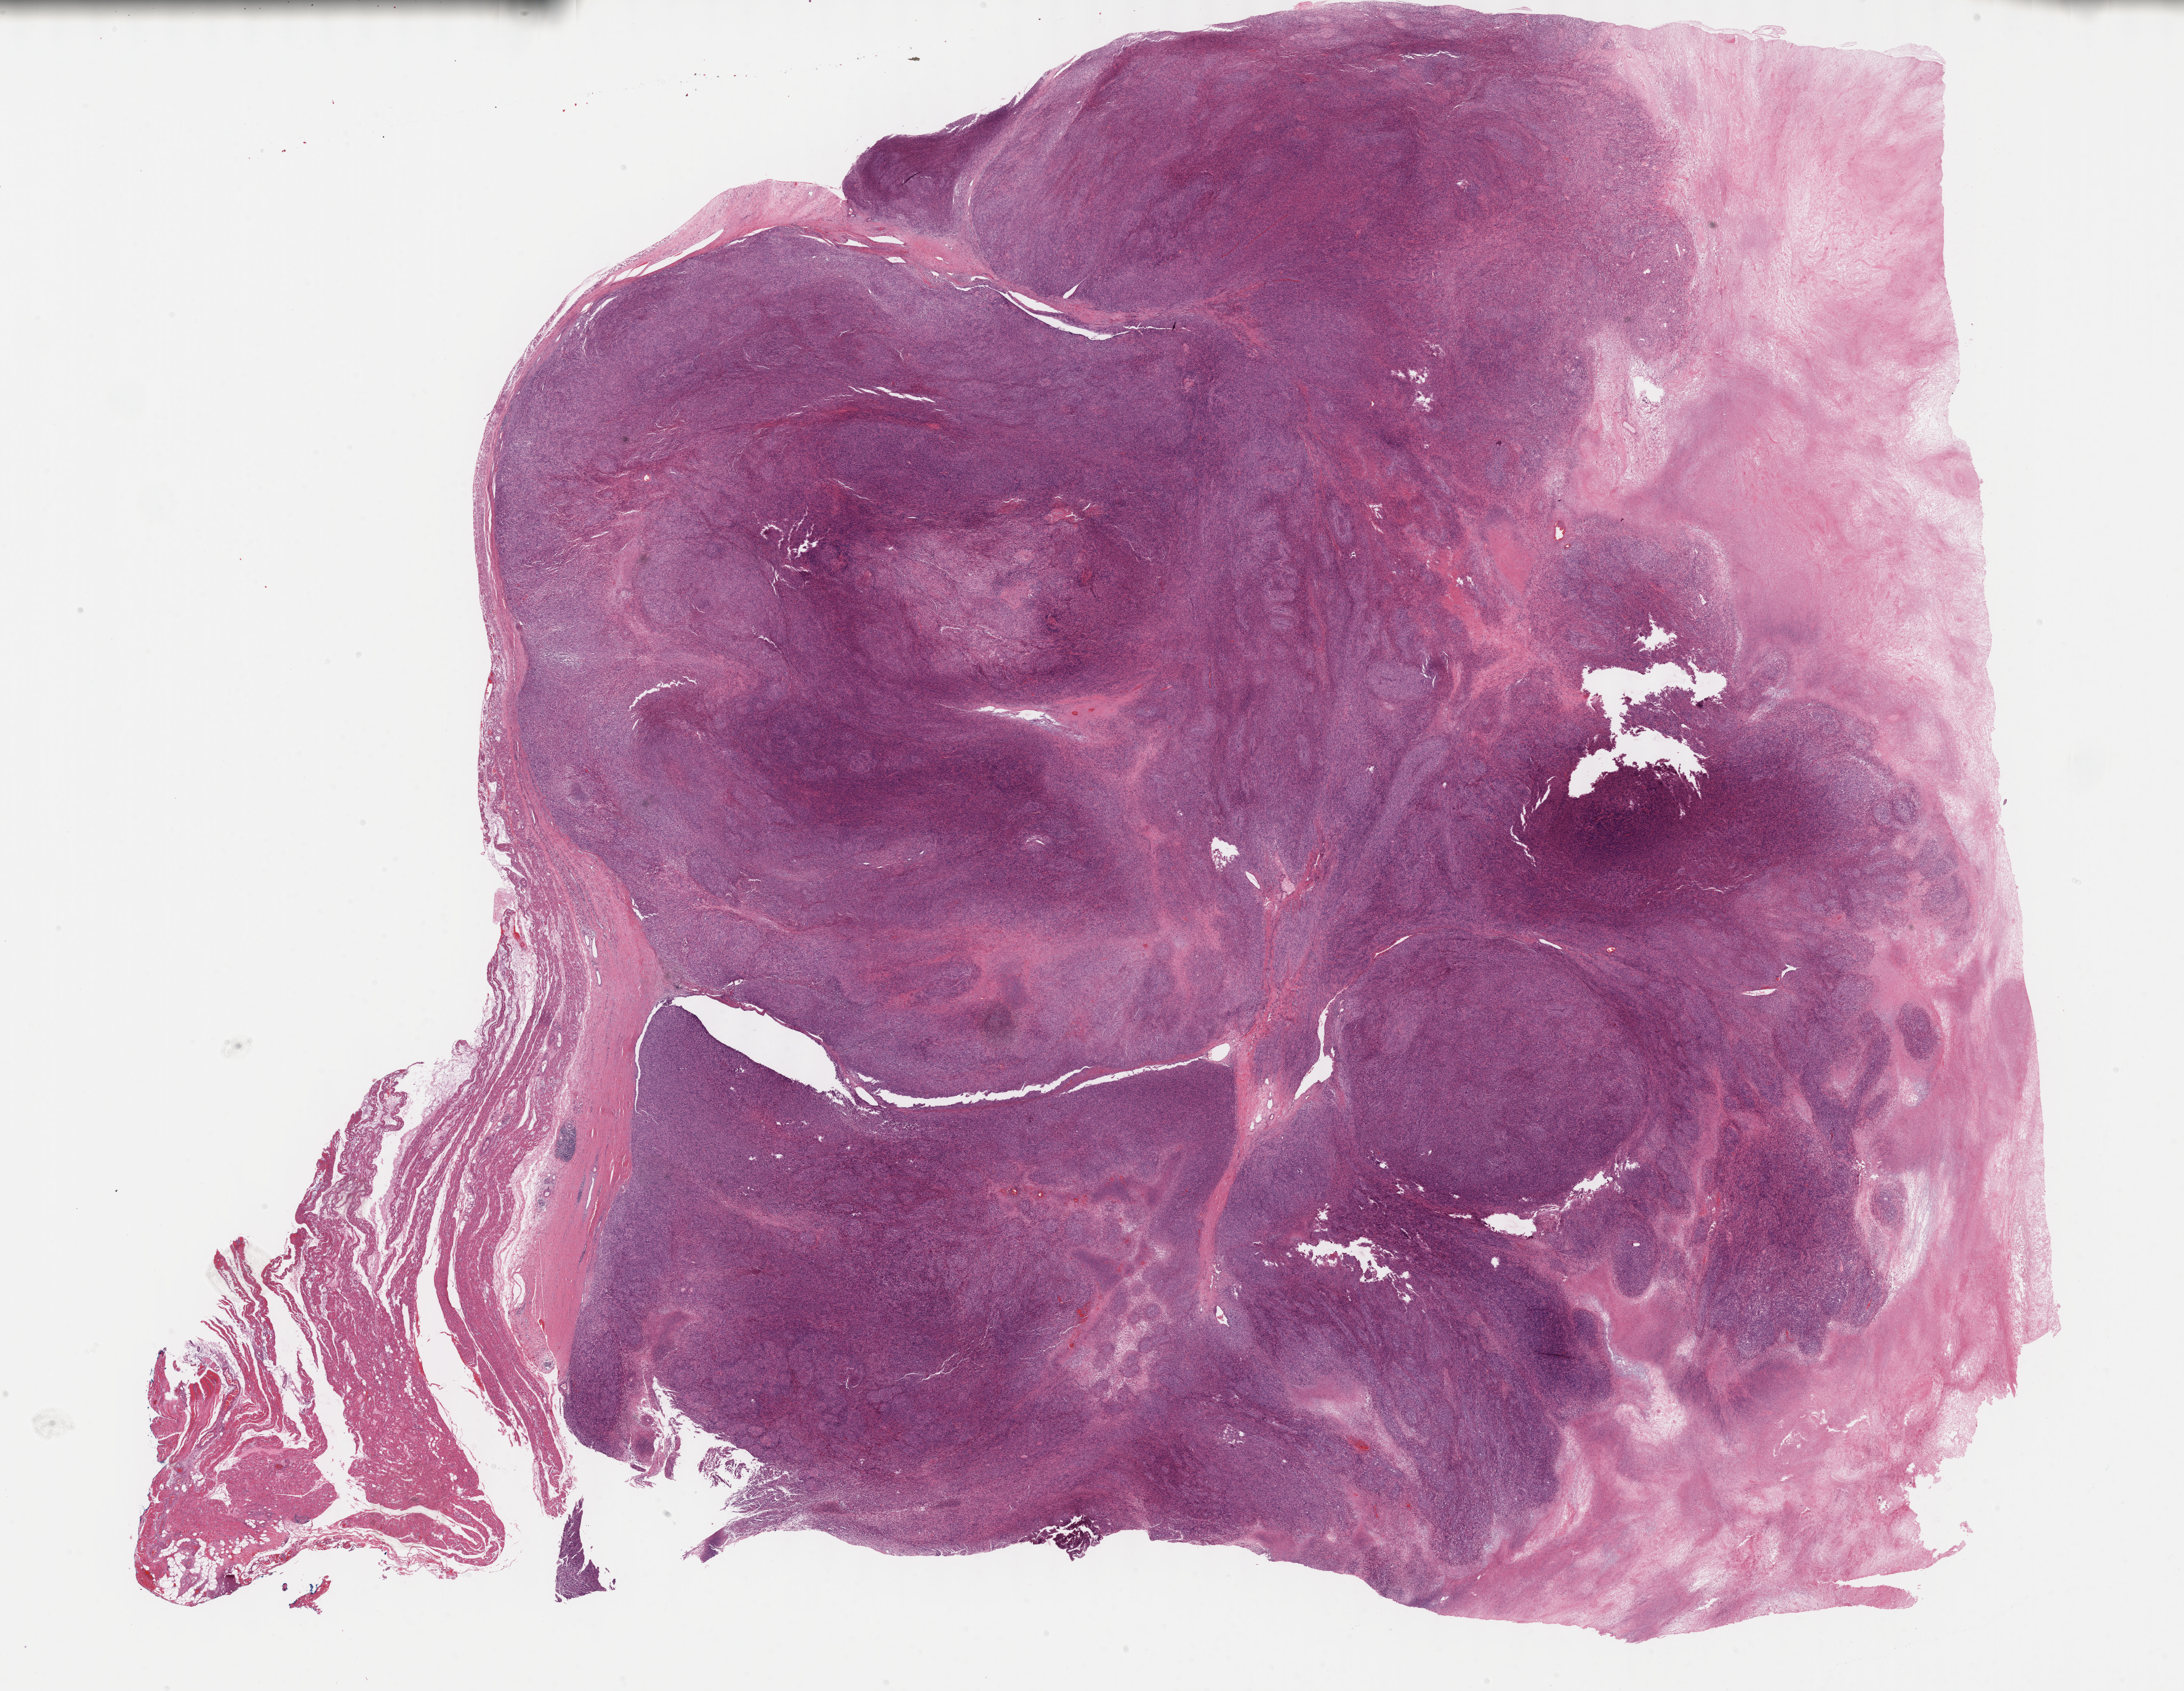
Whole-slide histology image, H&E-stained, whole scanned area (about 28.7 x 22.2 mm, from a 40x scan) shown as a low-resolution overview, FFPE section, sample: primary tumour, retroperitoneum and peritoneum. Male patient; age at initial diagnosis 55 years.
- pathologic diagnosis: Undifferentiated sarcoma